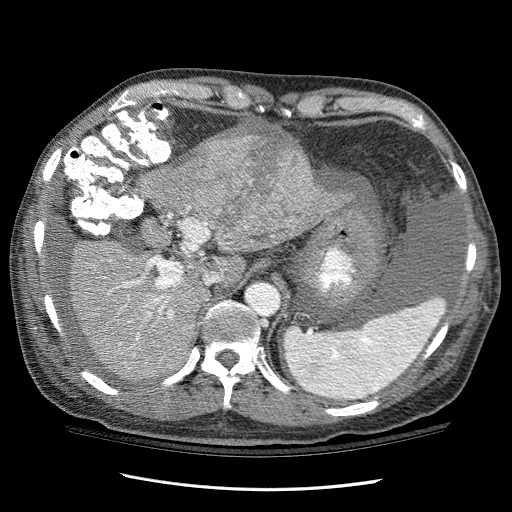
Contrast-enhanced abdominal CT (liver protocol), one axial slice; slice 79 of 114 in the series (ordered by position); reconstruction kernel STANDARD; one of 3 acquisitions stored at this slice position; soft-tissue window (W 400 / L 40 HU); 2.5 mm slice thickness; 512 × 512 image matrix. From the clinical record (not read from this slice): diagnosis: hepatocellular carcinoma (patient treated with transarterial chemoembolisation; whether this scan precedes or follows treatment is not stated here); TNM stage (as recorded): Stage-I; Child-Pugh class: C; tumour differentiation: well differentiated.
Outlined on this slice (semi-automatically segmented with operator editing):
- liver parenchyma outside the tumour (the mass and vessels are separate outlines, so this box may not span the whole liver): box from (x=70, y=158) to (x=338, y=379) px
- mass: (x=194, y=123)–(x=315, y=241)
- liver vessels: (x=103, y=260)–(x=173, y=345)